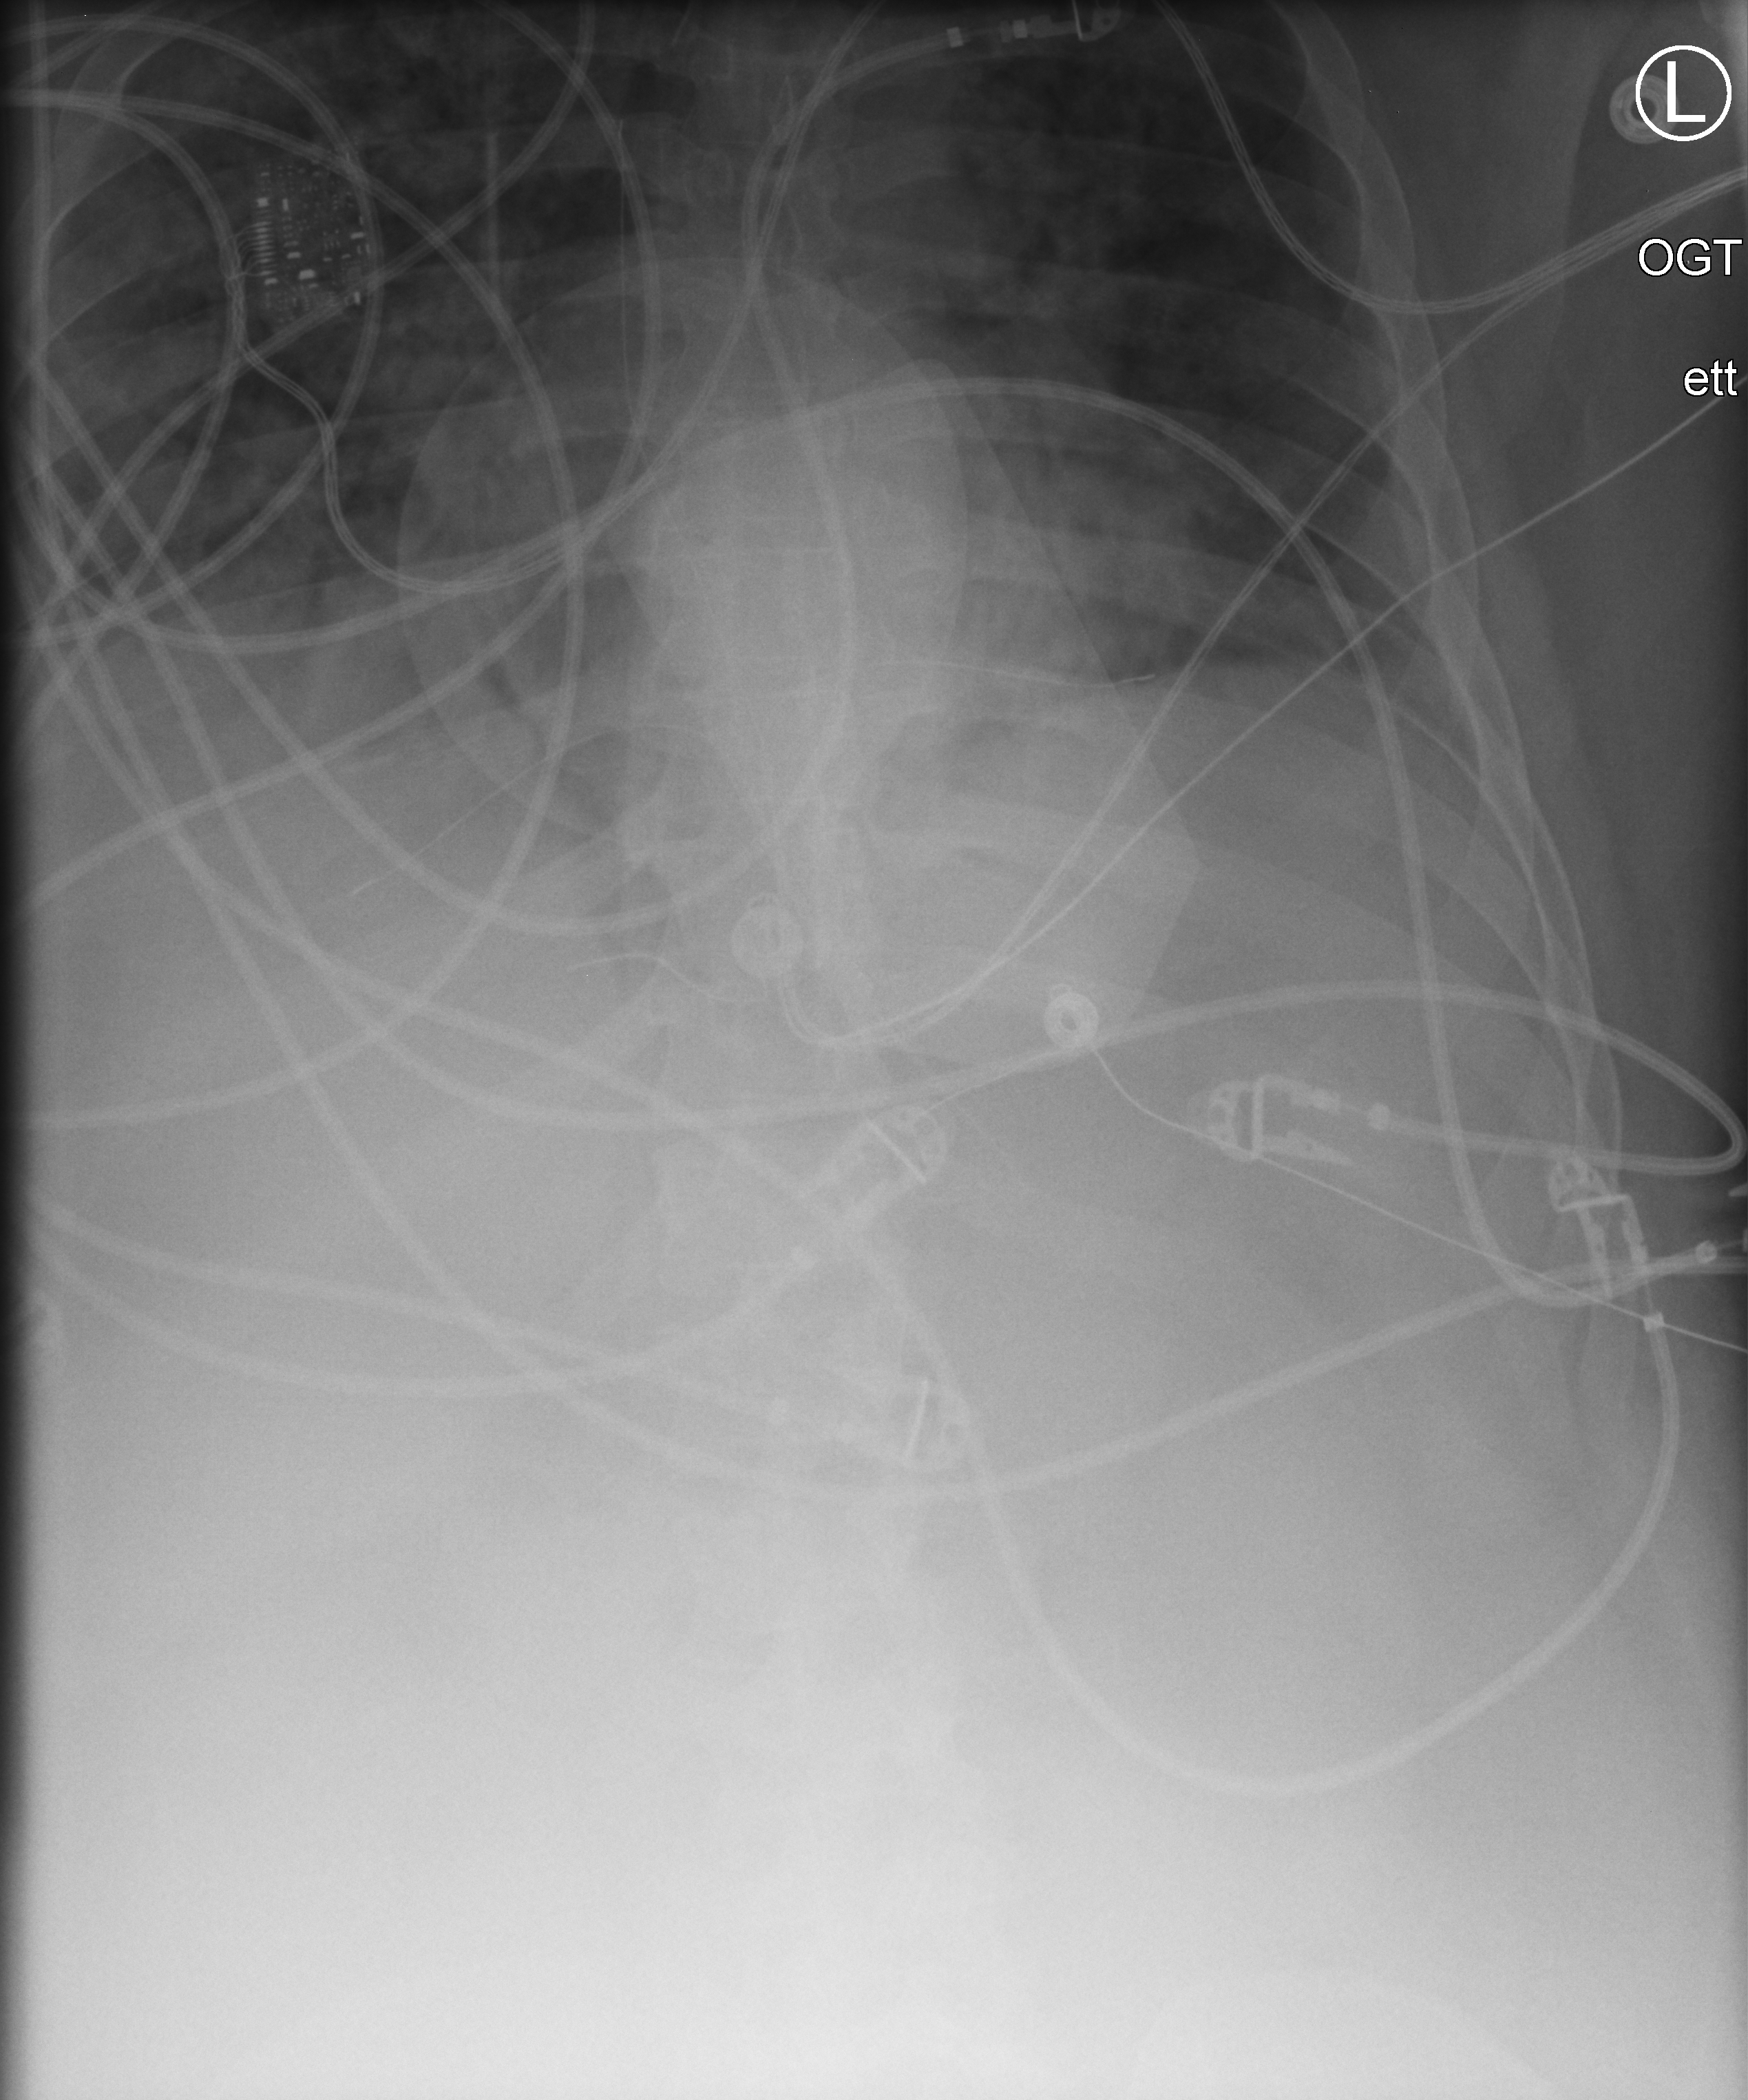
Chest X-ray (portable), anteroposterior (AP) projection. Patient hospitalised with COVID-19, aged 18–59 years.
From the hospital-stay record, not from the radiograph (when in the stay this image was taken is not recorded):
- mechanically ventilated during this hospital stay: yes
- admitted to intensive care during this hospital stay: yes